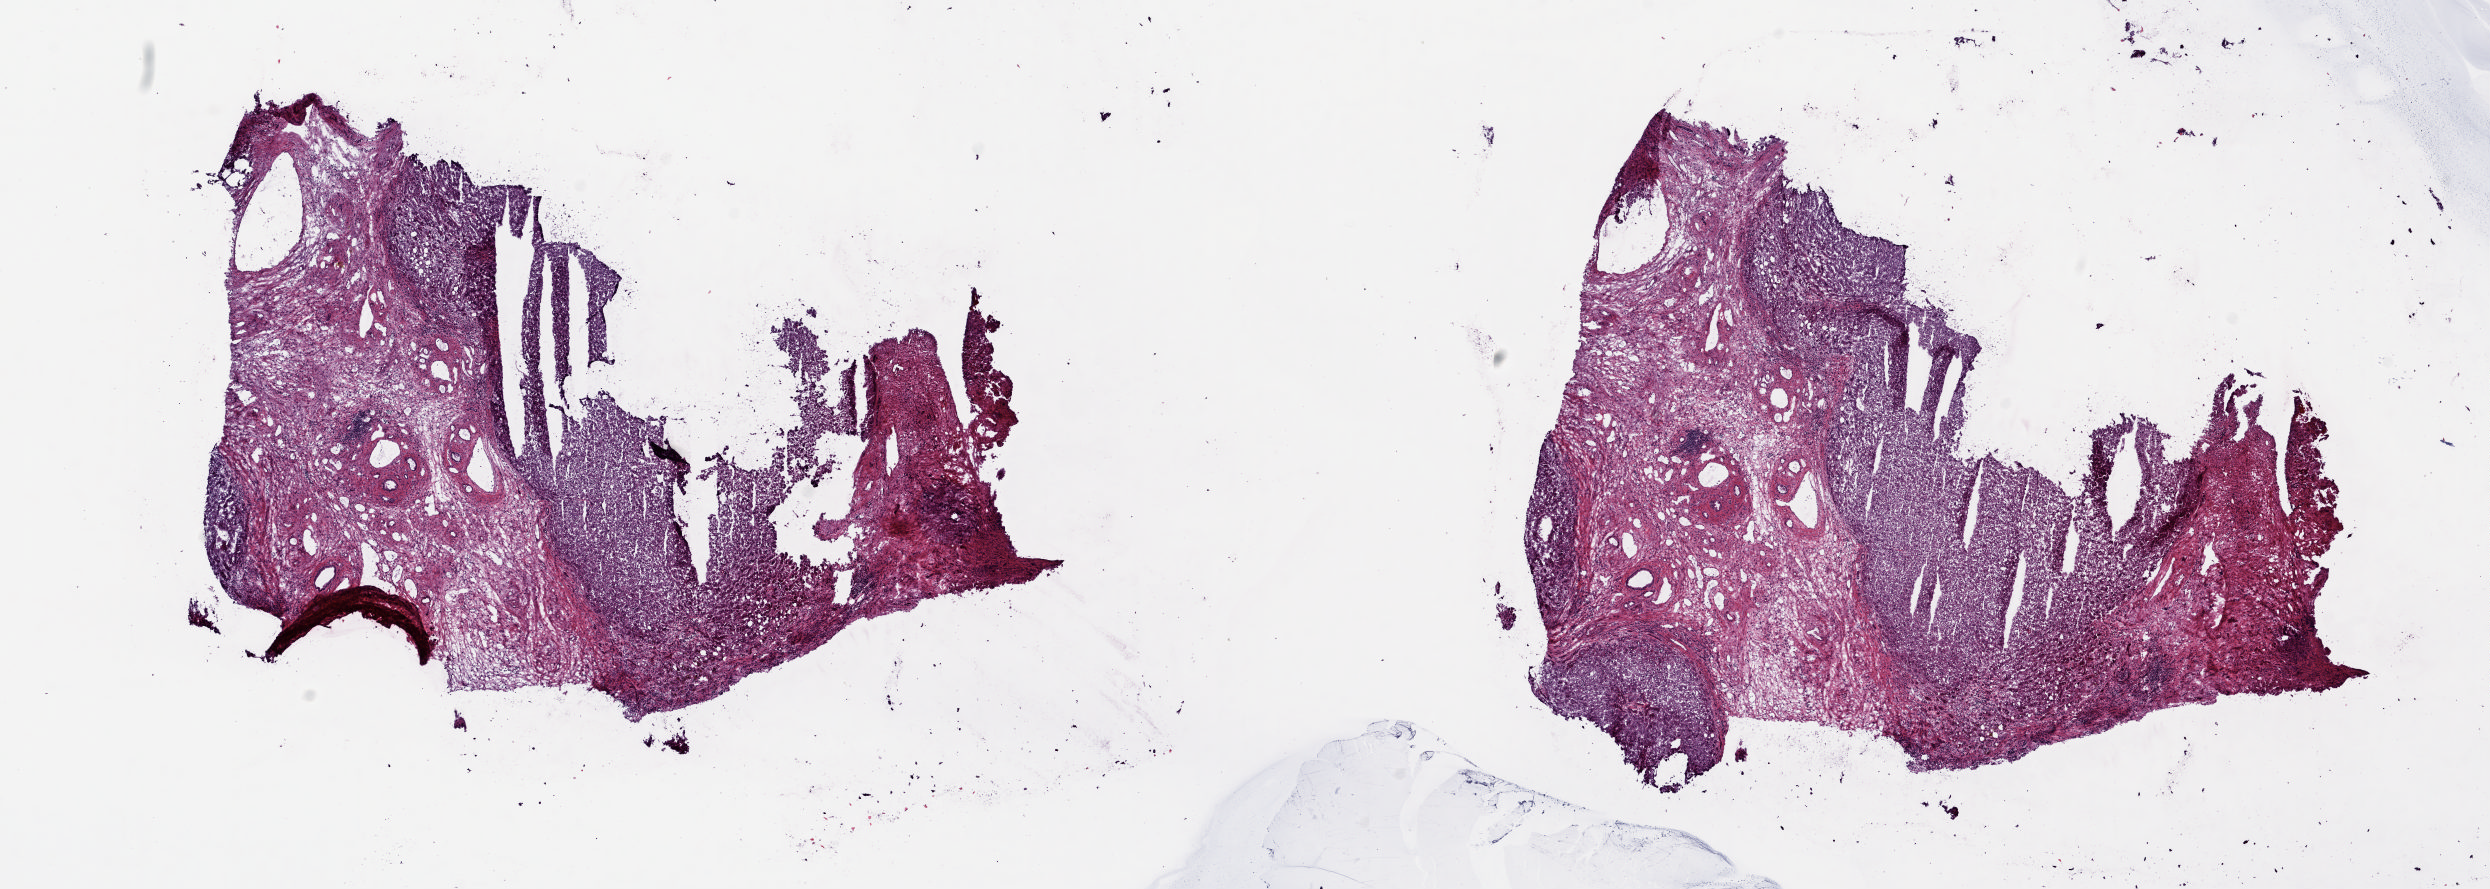
Whole-slide histology image, H&E — low-resolution overview of the scanned area, about 19.8 x 7.1 mm; frozen section from the top of the tissue portion; solid tissue normal (non-tumour tissue) sample from the liver. Patient: male, age at initial diagnosis 73 years. Composition of this section per pathologist review: tumour cells 0%, tumour nuclei 0%, normal cells 60%, stromal cells 40%, necrosis 0%. Inflammatory infiltration, as recorded: lymphocyte infiltration 10%, monocyte infiltration 0%, neutrophil infiltration 0%.
This section: solid tissue normal (non-tumour) sample from the same patient. Patient diagnosis: Hepatocellular carcinoma, NOS.